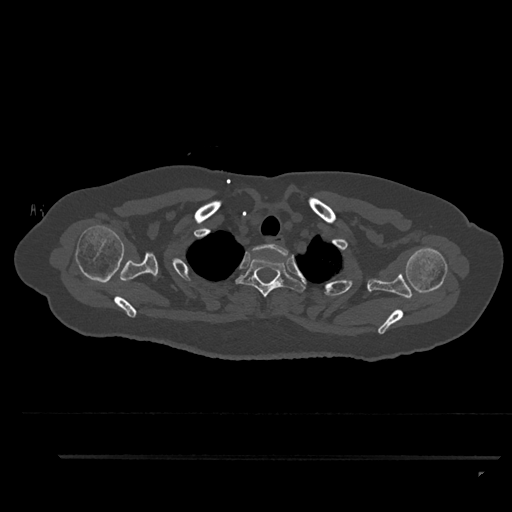
CT including the spine, one axial slice; slice 730 of 797 in the series (ordered by position); 120 kVp; bone window (W 1800 / L 400 HU); 0.5 mm slice thickness; 512 × 512 image matrix. Female patient, age 44 years. From the clinical record (not read from this slice): primary cancer: renal.
Annotated regions visible in this slice (semi-automatic segmentation, software-assisted and operator-edited):
- T1 vertebra: bounding box <250,244,289,259> (left, top, right, bottom; pixels)
- T2 vertebra: <235,257,306,297>